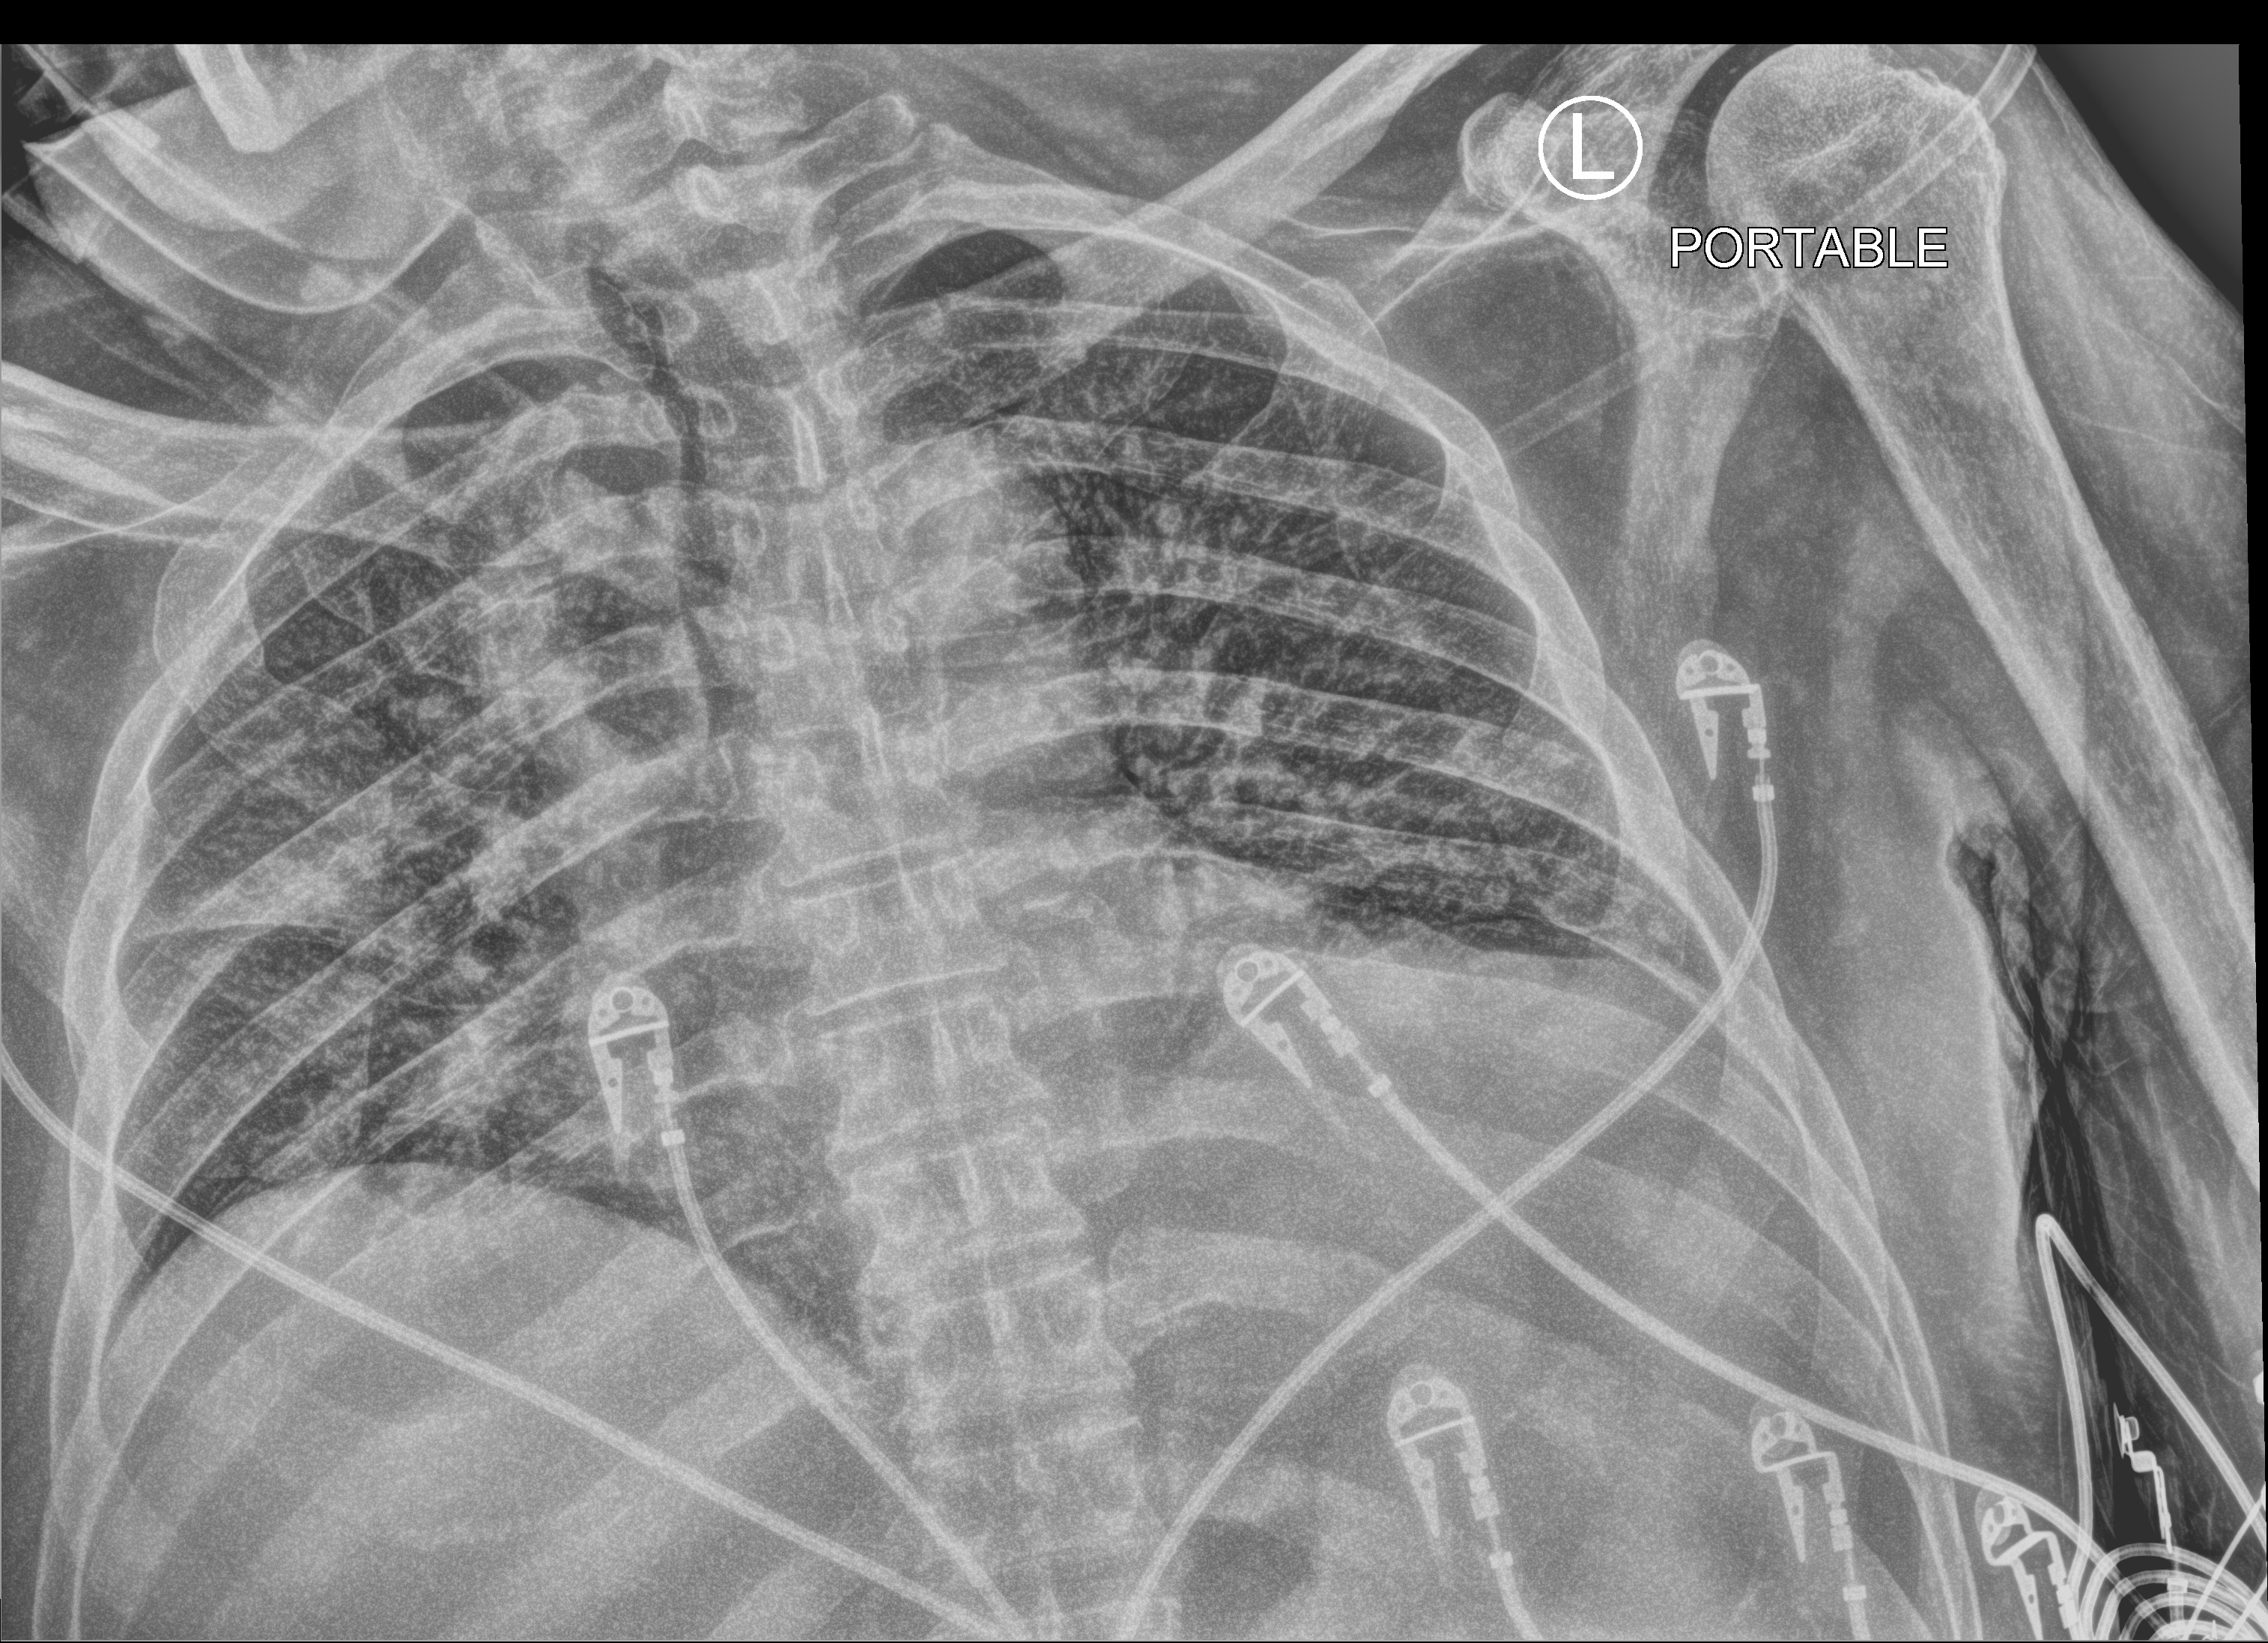
Portable chest radiograph, anteroposterior (AP) projection. Male patient hospitalised with COVID-19, age 60–74 years.
Hospital-stay facts (about this admission, not read from this image; timing relative to this image not recorded):
- admitted to intensive care during this hospital stay: no
- mechanically ventilated during this hospital stay: no